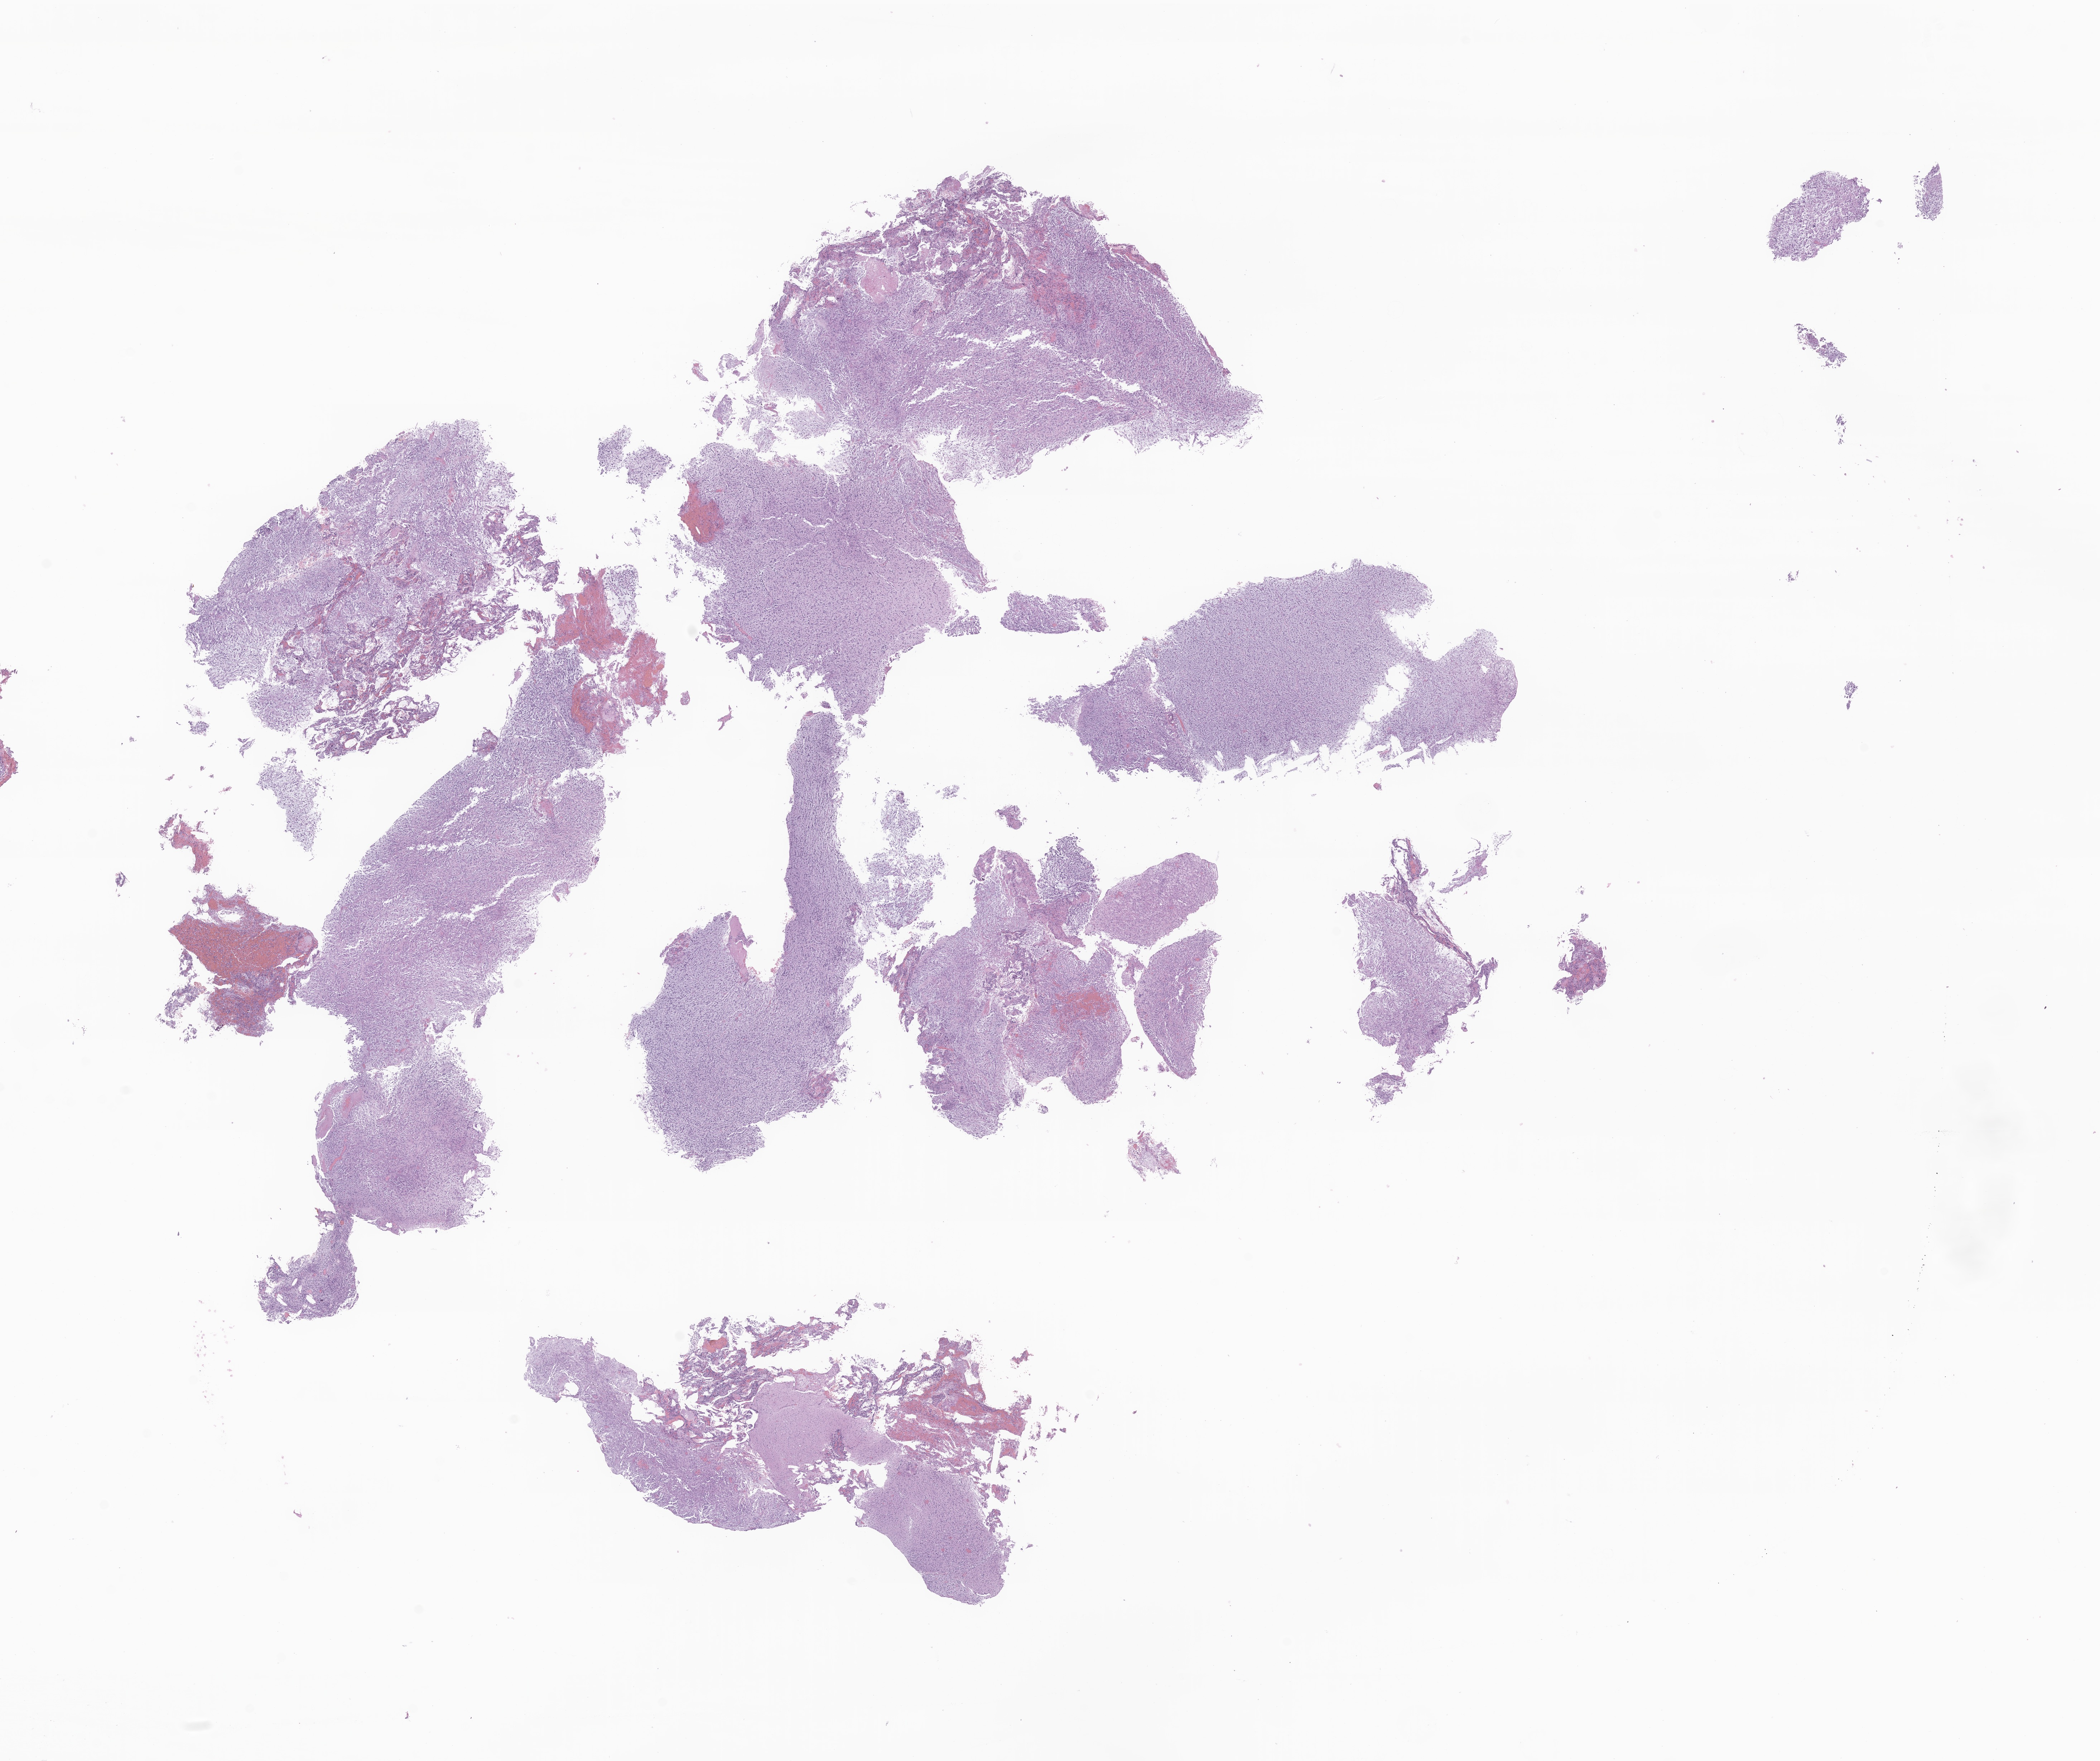
H&E whole-slide image of tumor tissue from the brain, a low-resolution overview of the entire scanned area, about 24.7 x 20.7 mm. FFPE section. Patient male; age 139 months (11 years 7 months).
• recorded diagnosis: Neoplasm, malignant